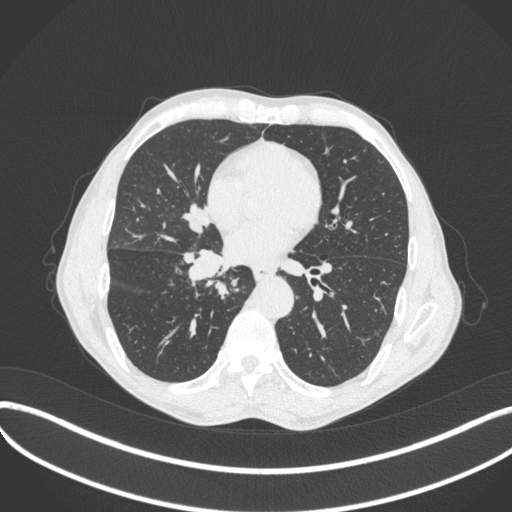
Chest CT, one axial slice. Position 196 of 481 along the scan axis. Reconstruction kernel B31f. 120 kVp. Lung window (W 1500 / L -600 HU). 1 mm slice thickness. 512 × 512 image matrix, field of view 400 × 400 mm. Male patient, age 65 years. Case-level facts recorded for this patient, not image findings: clinical TNM (as recorded): T2a N0 M0; histopathological grade: G2.
Annotated regions visible in this slice (rectangle marked by the reading radiologist):
- lung tumour (recorded histology: squamous cell carcinoma): bounding box <171,246,233,287> (left, top, right, bottom; pixels)